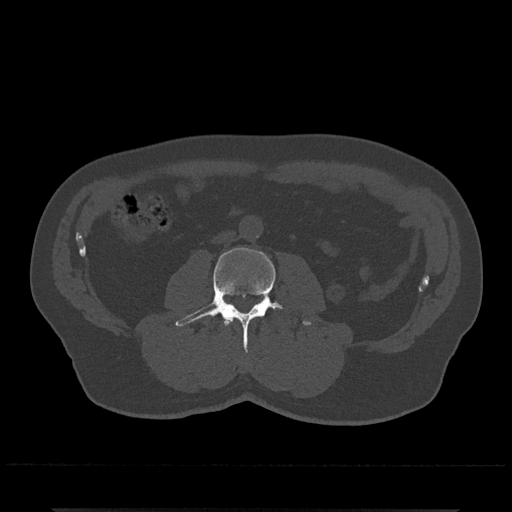
CT including the spine, one axial slice. Slice 222 of 797 in the series (ordered by position). Reconstruction kernel Br40s/3. Bone window (W 1800 / L 400 HU). 0.5 mm slice thickness. 512 × 512 image matrix. Patient: male, 67 years. From the clinical record (not read from this slice): primary cancer: prostate.
Outlined on this slice (semi-automatic segmentation, software-assisted and operator-edited):
- L2 vertebra: bounding box (x1, y1, x2, y2) in pixels: (224, 318, 232, 325)
- L3 vertebra: (175, 247, 312, 351)